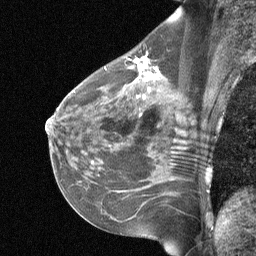
Breast MRI (dynamic contrast-enhanced), one sagittal slice. Dynamic contrast-enhanced study with each time point stored as its own series, time point 2 of 3 at this slice position (early post-contrast, ordered by acquisition time). 1.5 T. TE 4.8 ms, TR 27 ms. 2 mm slice thickness. 256 × 256 image matrix, field of view 200 × 200 mm. Patient: female, 51 years. Case-level facts recorded for this patient, not image findings: setting: breast cancer imaged before/during neoadjuvant chemotherapy; receptor status: HR-positive, HER2-negative.
Outlined on this slice (semi-automatic segmentation, software-assisted and operator-edited):
- analysis volume of interest (the breast-tissue region the enhancement analysis was run in; not a lesion): bounding box [x1, y1, x2, y2] px = [88, 42, 196, 119]
- tumour enhancement mask (voxels above the 90 % enhancement threshold inside the analysis volume of interest): [132, 56, 159, 91]